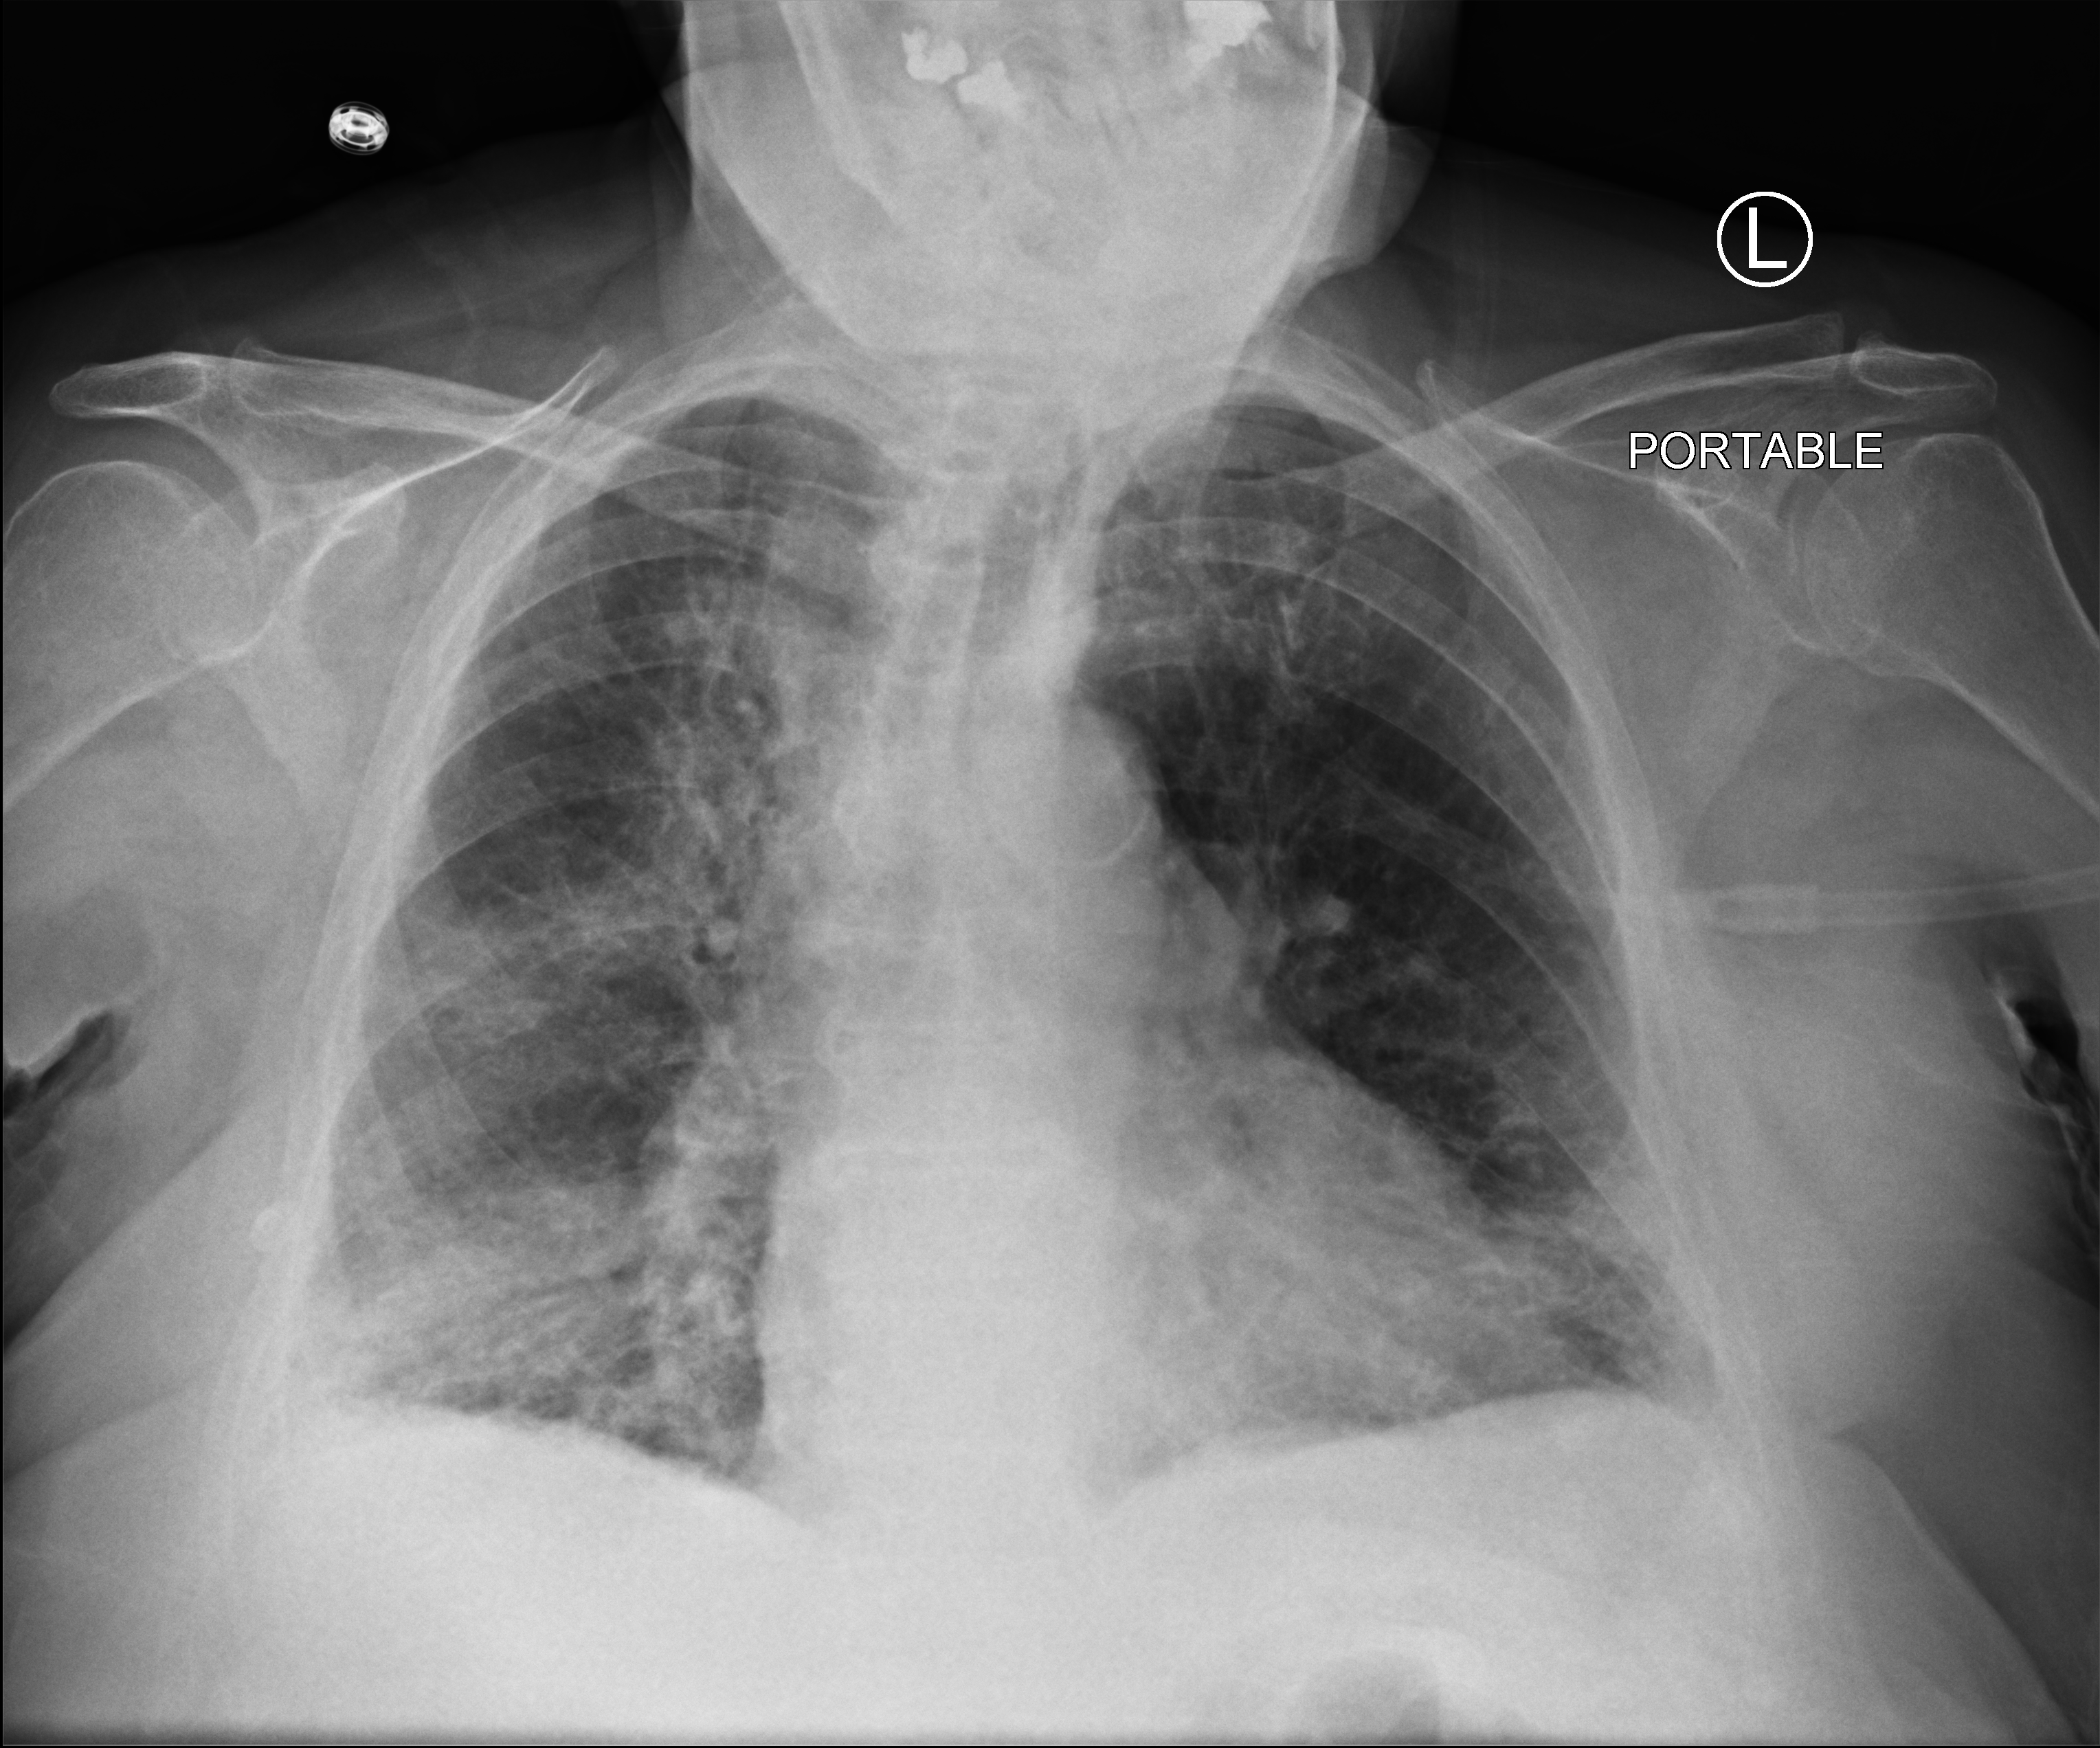
Portable chest radiograph; anteroposterior (AP) projection. Patient hospitalised with COVID-19; female, aged 75–90 years.
Hospital-stay facts (about this admission, not read from this image; timing relative to this image not recorded):
- COPD (admission record): no
- mechanically ventilated during this hospital stay: no
- admitted to intensive care during this hospital stay: no